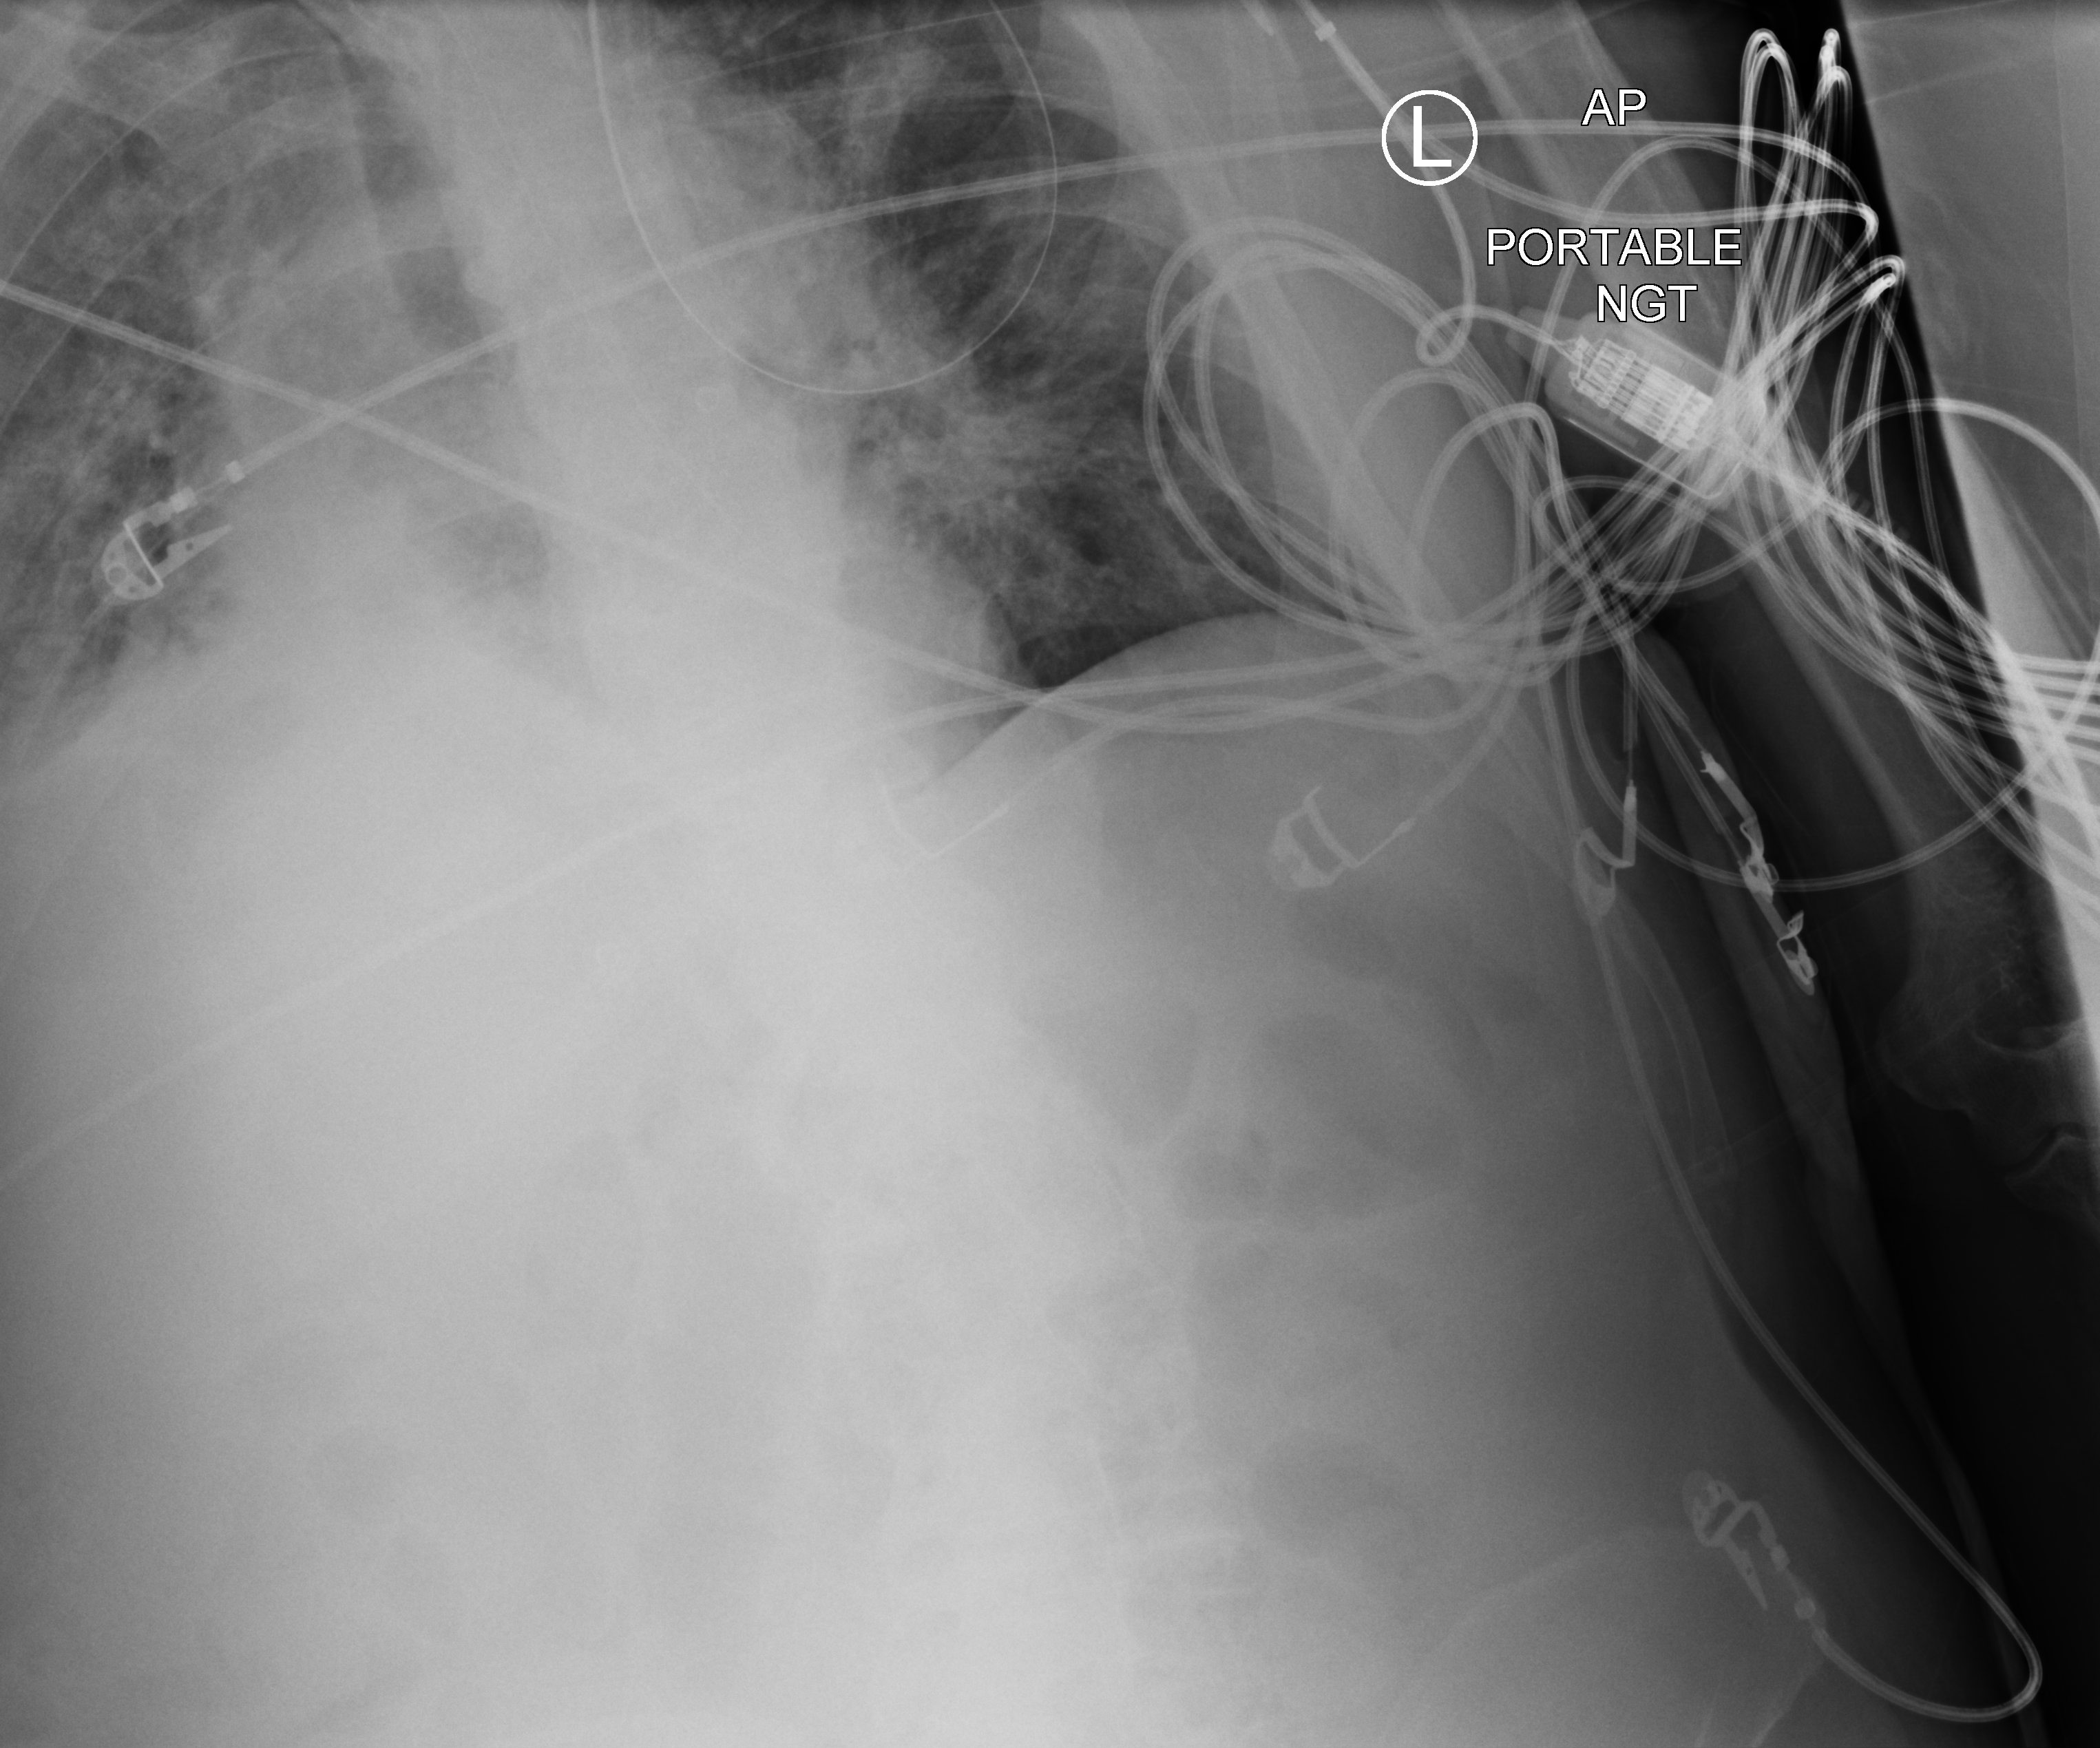
Portable chest radiograph; anteroposterior (AP) projection. Male patient hospitalised with COVID-19, age 75–90 years.
Admission-level facts for this patient (not findings on this image; timing relative to this image not recorded): admitted to intensive care during this hospital stay: no.